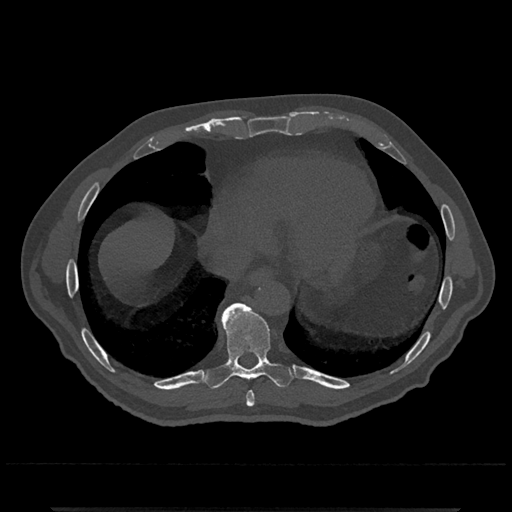
CT including the spine, one axial slice. Position 619 of 797 along the scan axis. Reconstruction kernel Br40s/3. 120 kVp. Bone window (W 1800 / L 400 HU). 512 × 512 image matrix. Male patient, age 67 years. From the clinical record (not read from this slice): primary cancer: prostate.
Structures marked on this image (semi-automatic segmentation, software-assisted and operator-edited):
- T8 vertebra: box from (x=246, y=391) to (x=255, y=407) px
- T9 vertebra: (x=204, y=303)–(x=295, y=389)